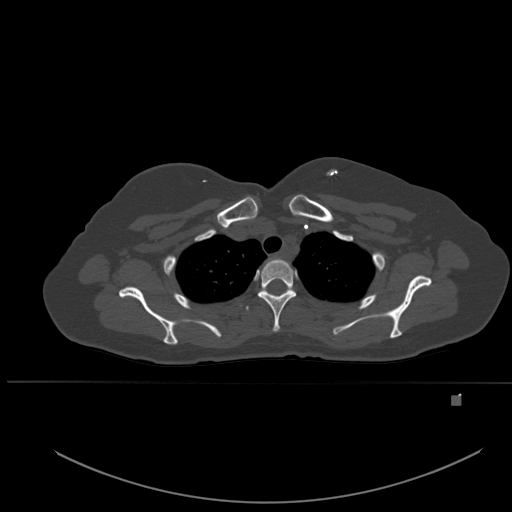
CT including the spine, one axial slice; slice 405 of 651 in the series (ordered by position); bone window (W 1800 / L 400 HU); 512 × 512 image matrix, field of view 443 × 443 mm. Female patient, age 49 years. From the clinical record (not read from this slice): primary cancer: breast; vertebrae with lytic lesions (as recorded): L3, T12, L4.
Structures marked on this image (semi-automatically segmented with operator editing):
- T1 vertebra: bounding box (x1, y1, x2, y2) in pixels: (266, 260, 290, 267)
- T2 vertebra: (258, 258, 296, 332)
- T3 vertebra: (246, 289, 291, 310)